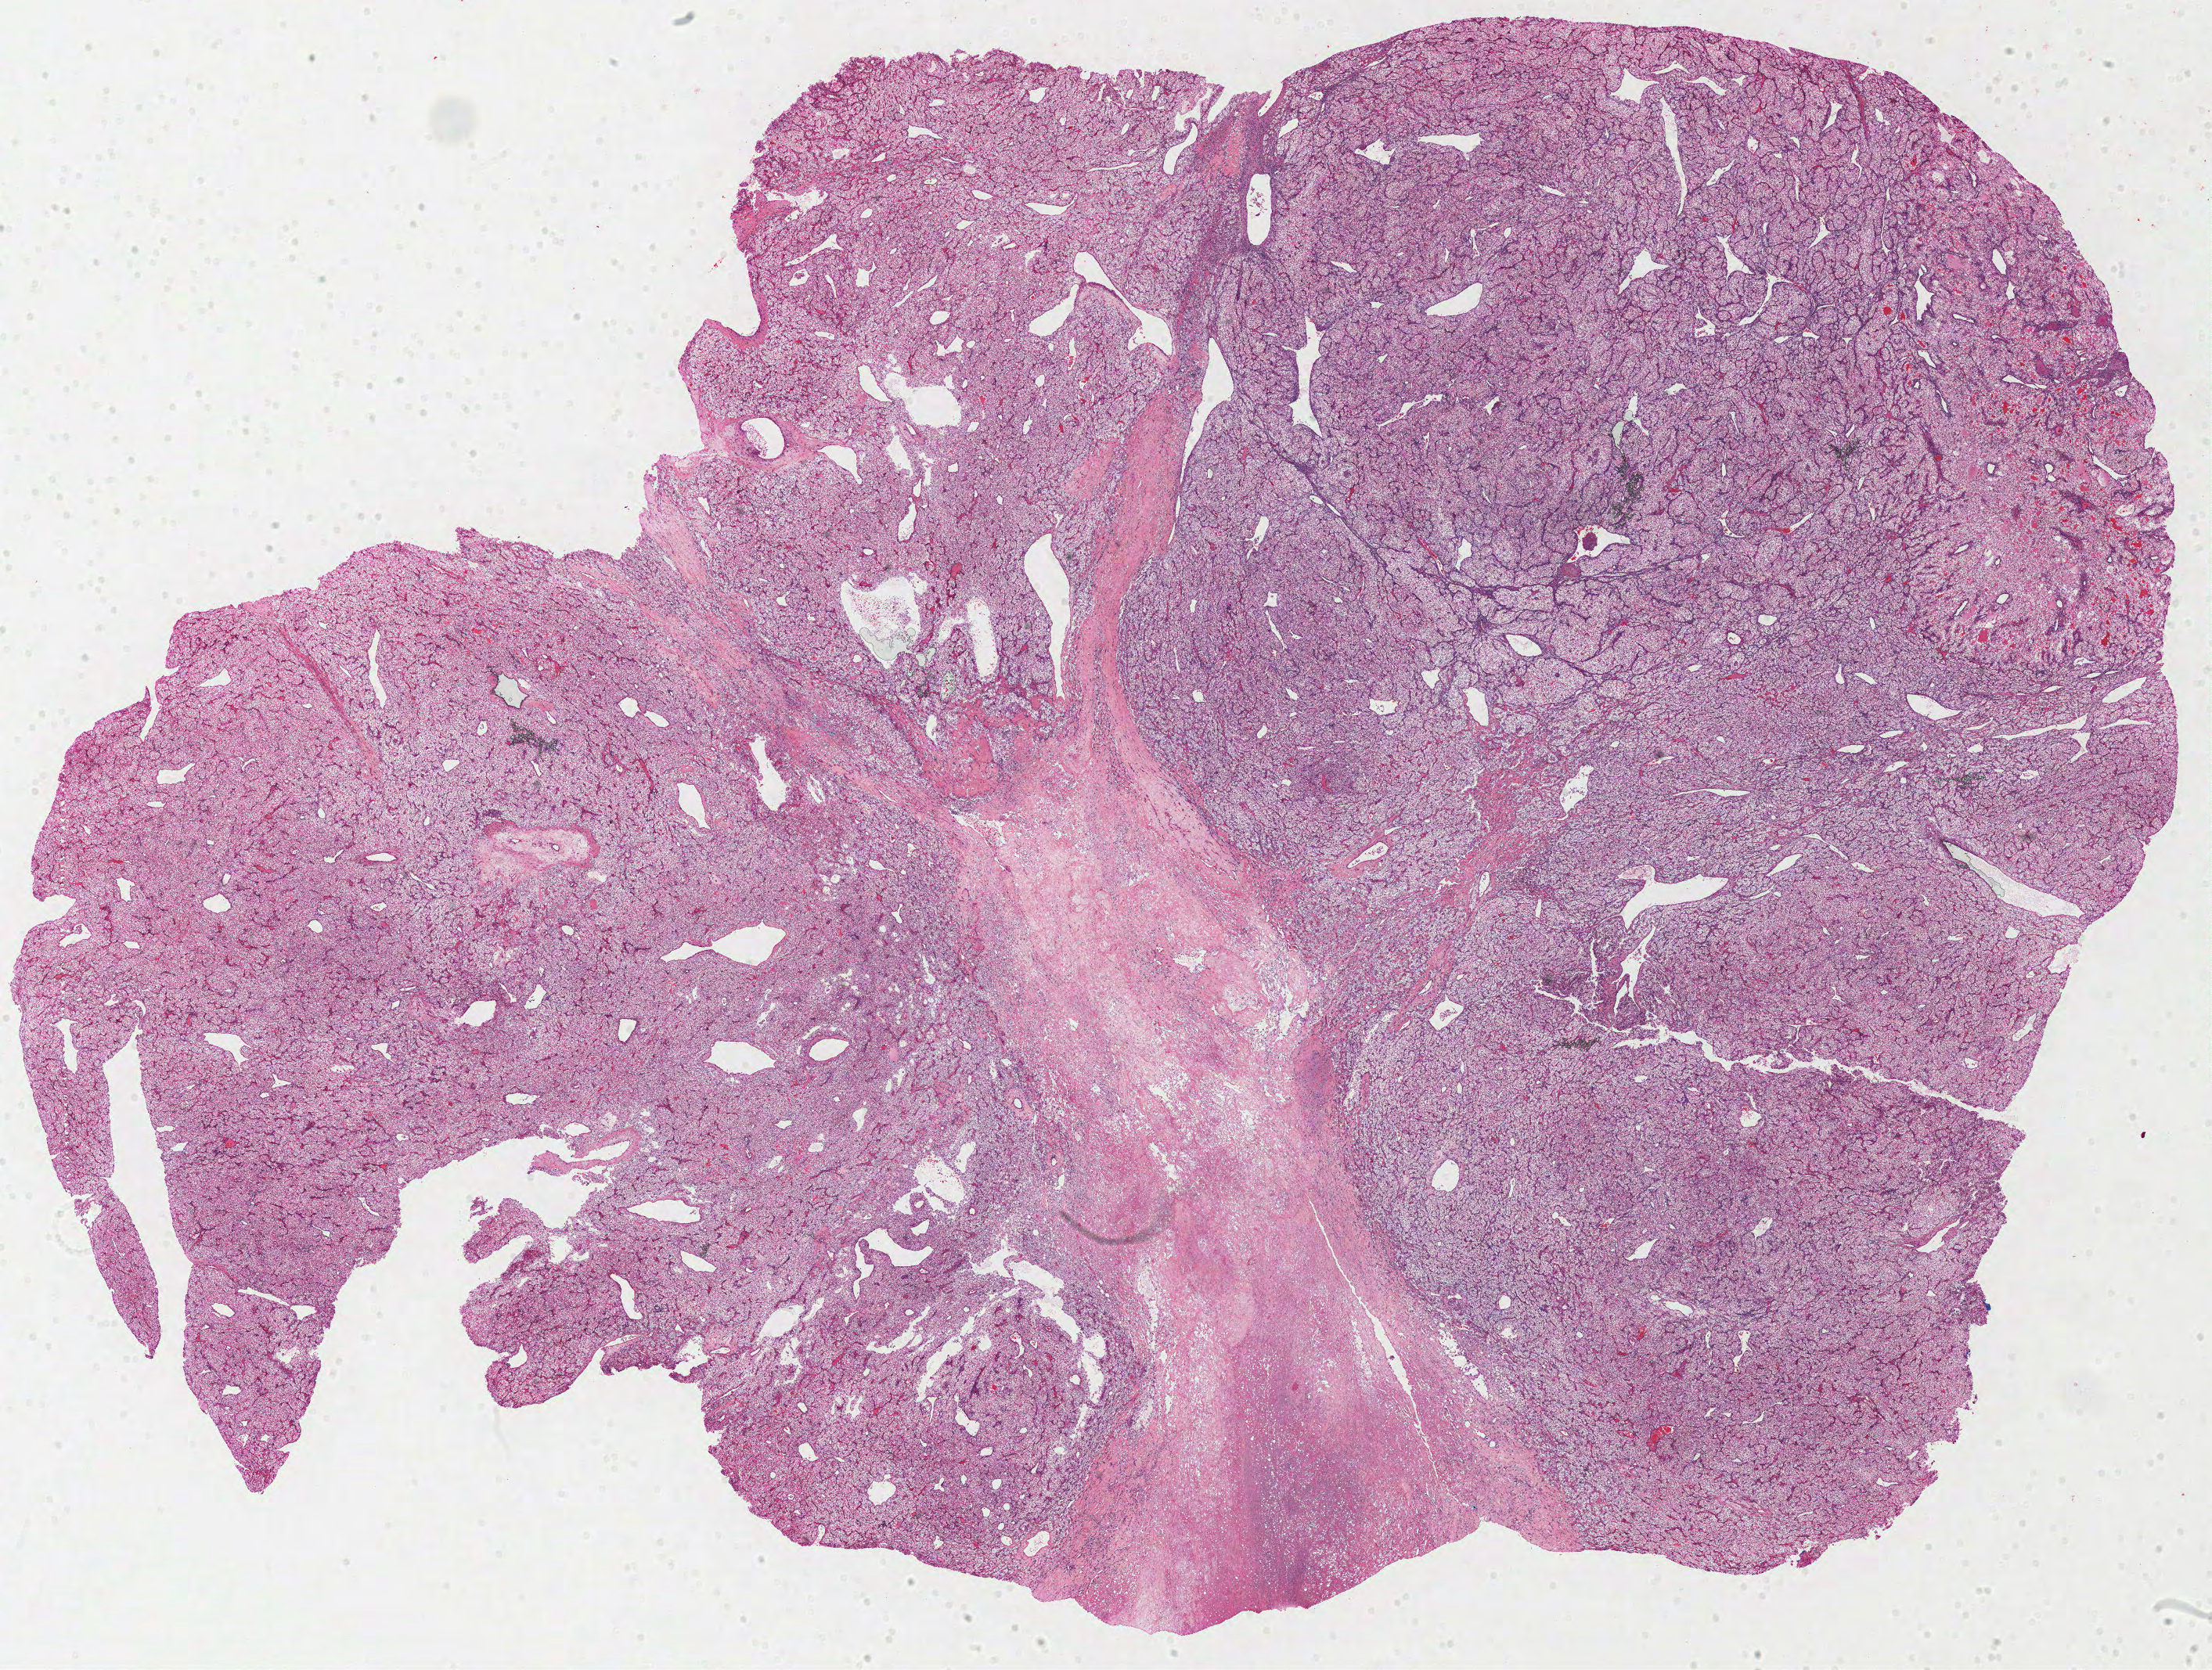
Digitized H&E tissue section (whole slide), shown as a low-resolution overview of the whole scanned area (about 22.3 x 16.8 mm, from a 40x scan). FFPE section. Kidney, primary tumour sample. Male, age 57 years at initial diagnosis. Histologic grade: G3 (poorly differentiated).
Histologic diagnosis: Clear cell adenocarcinoma, NOS. Laterality: left. AJCC pathologic stage: IV.